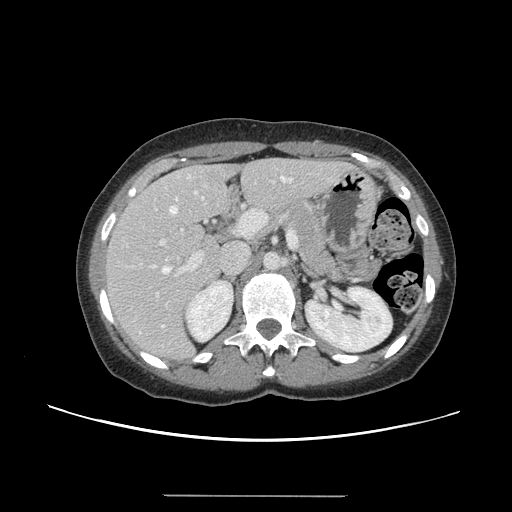
Contrast-enhanced abdominal CT, one axial slice; 120 kVp; intravenous contrast given; soft-tissue window (W 400 / L 40 HU); 2.5 mm slice thickness; 512 × 512 image matrix, field of view 380 × 380 mm. Female patient, age 53 years. Case-level facts recorded for this patient, not image findings: diagnosis: colorectal cancer liver metastases, imaged before liver resection; multiple liver metastases: yes; largest metastasis: 1.1 cm; disease in both lobes: no.
Outlined on this slice (expert manual segmentation):
- hepatic veins: bounding box [x1, y1, x2, y2] px = [162, 177, 292, 327]
- liver: [107, 159, 345, 360]
- planned liver remnant (the part of the liver to remain after resection): [108, 159, 316, 298]
- portal vein (with intrahepatic branches): [131, 206, 298, 297]